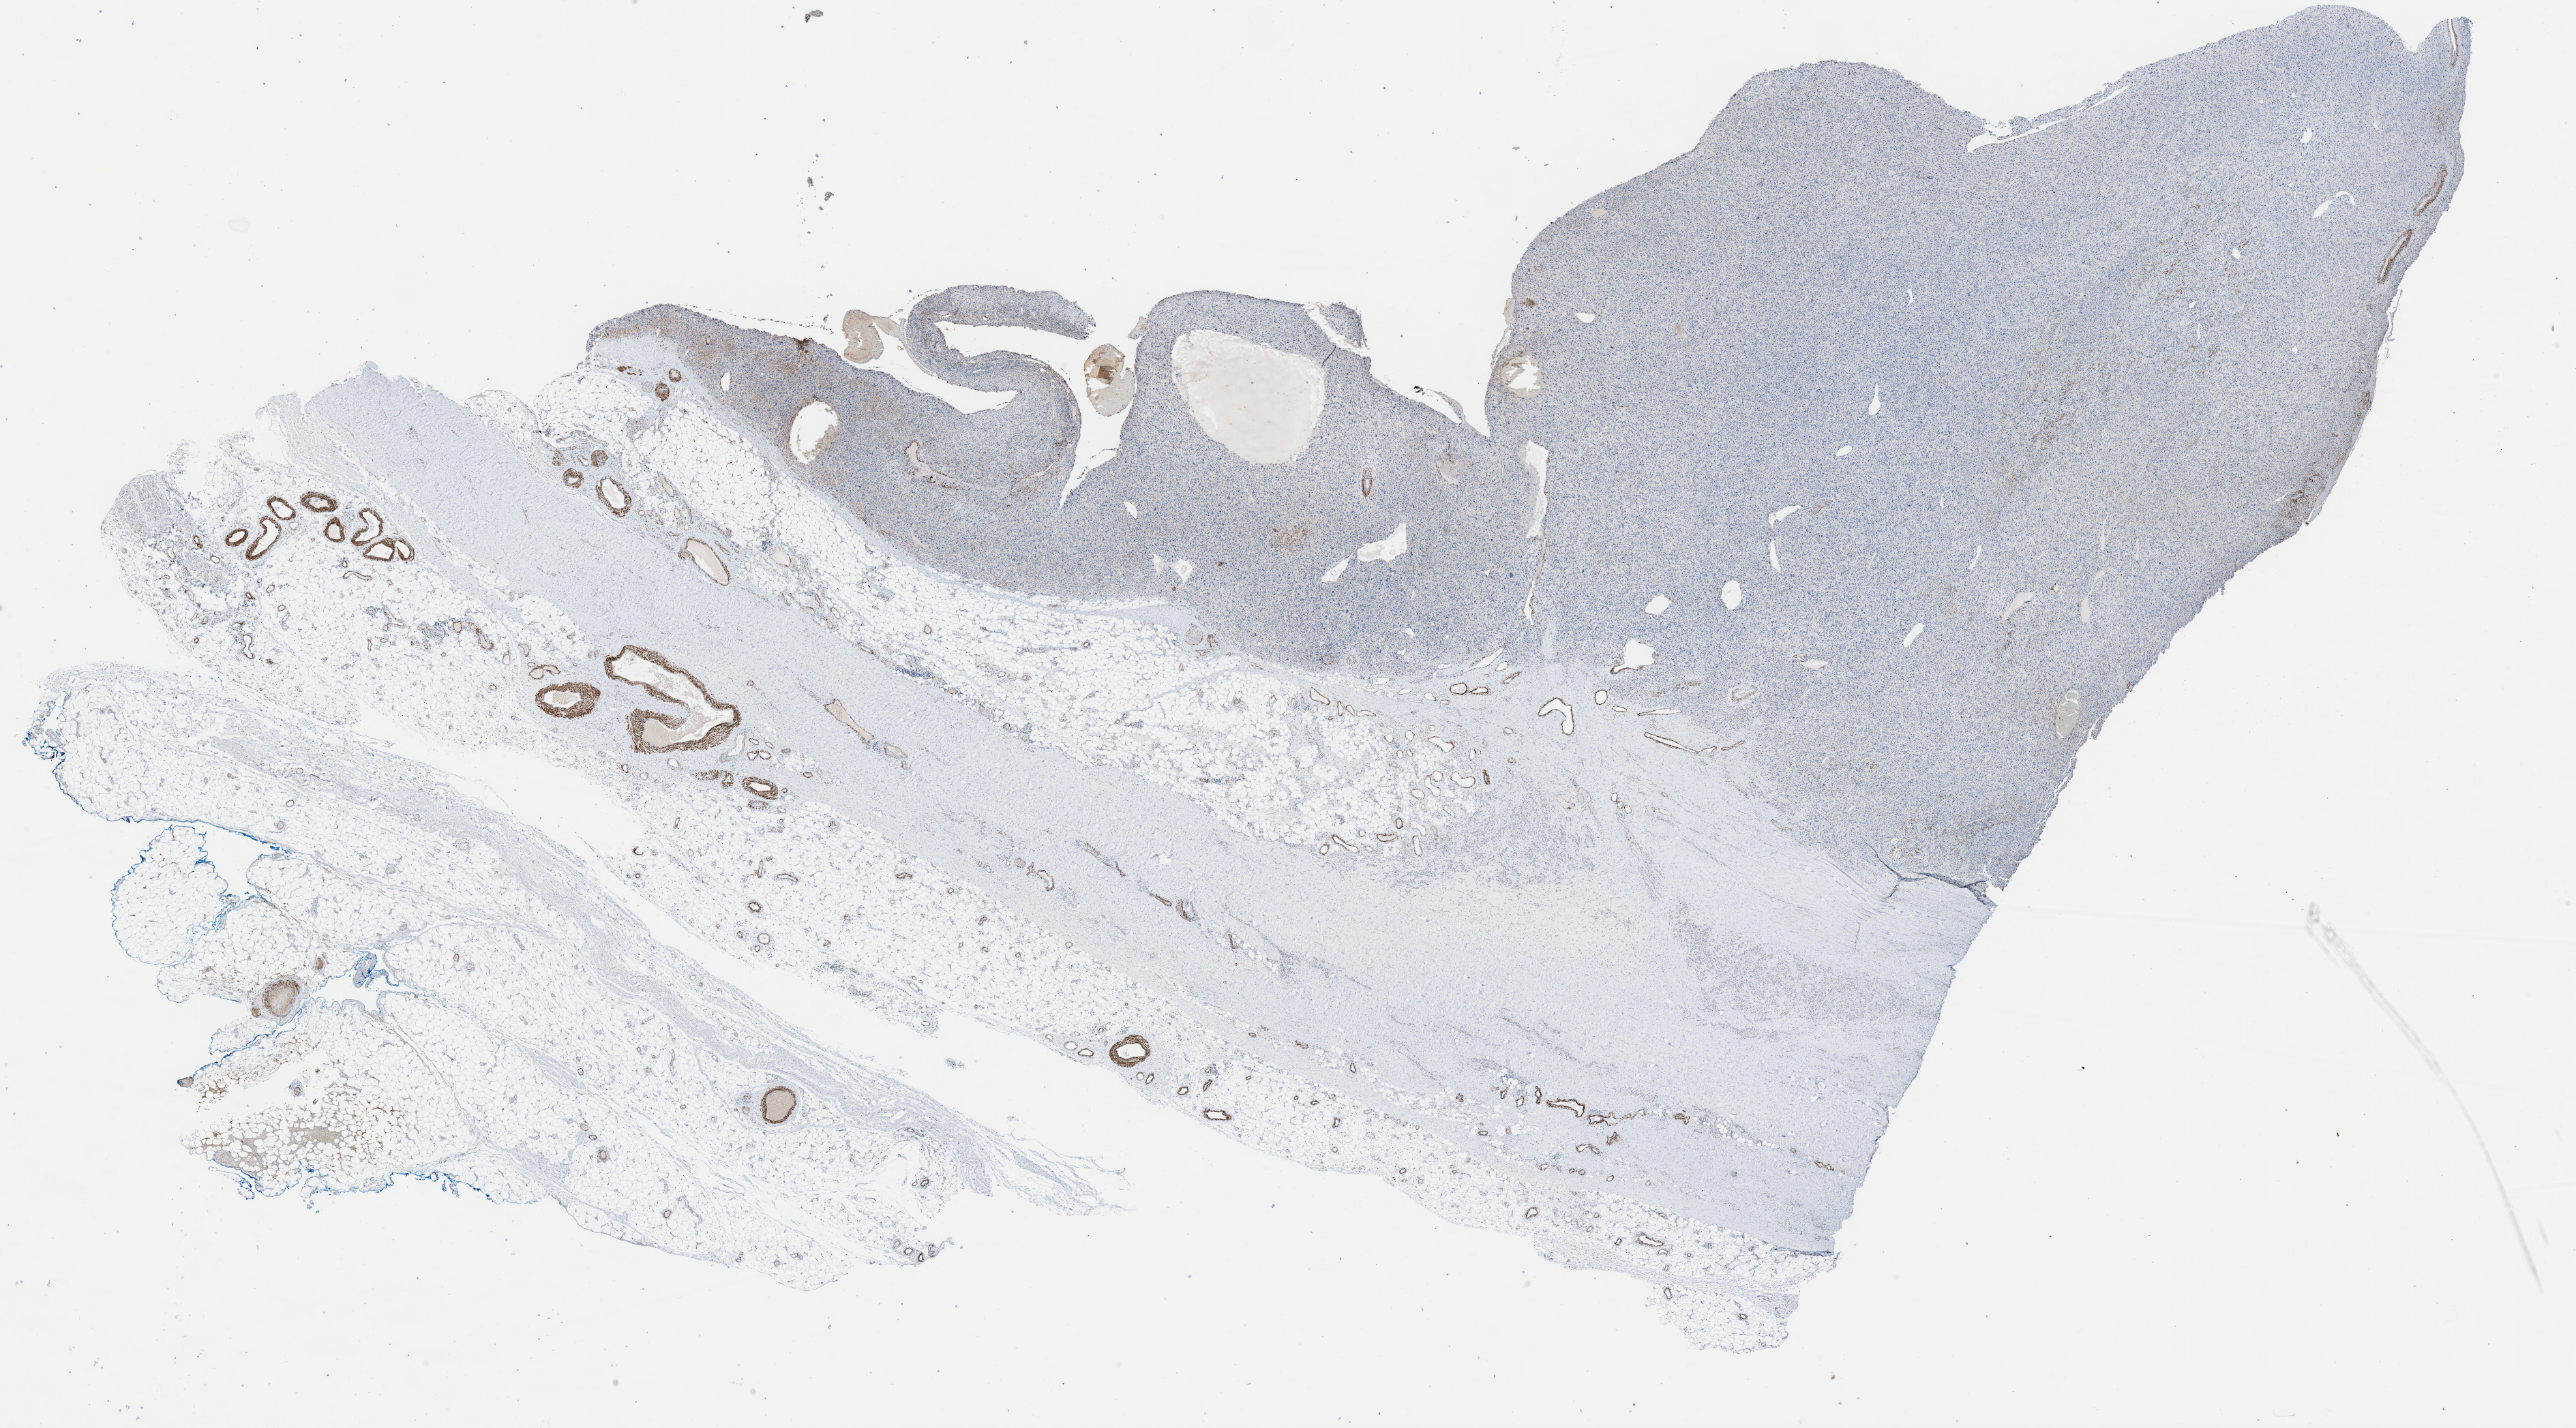
Whole-slide histology image, H&E-stained, shown as a low-resolution overview of the whole scanned area (about 29.8 x 16.5 mm, from a 40x scan), formalin-fixed paraffin-embedded (FFPE) diagnostic section, connective, subcutaneous and other soft tissues, primary tumour sample. Female patient; age at initial diagnosis 75 years.
Pathologic diagnosis: Malignant fibrous histiocytoma (connective, subcutaneous and other soft tissues of lower limb and hip).